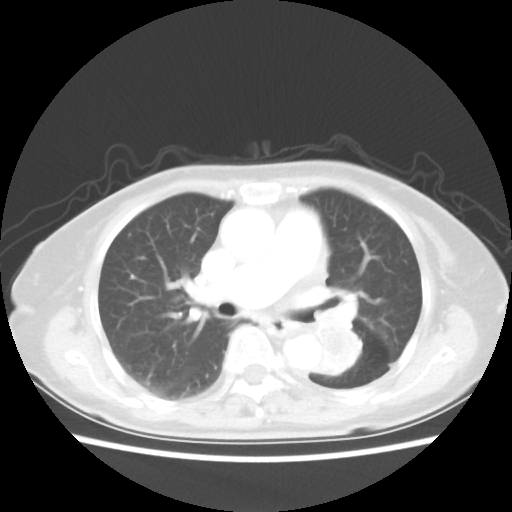
Chest CT, one axial slice. Position 29 of 50 along the scan axis. 80 kVp. Lung window (W 1500 / L -600 HU). 512 × 512 image matrix, field of view 335 × 335 mm. Patient: female, 81 years. From the clinical record (not read from this slice): clinical TNM (as recorded): T2 N0 M1a.
Structures marked on this image (rectangle marked by the reading radiologist):
- lung tumour (recorded histology: squamous cell carcinoma): bounding box <313,321,366,379> (left, top, right, bottom; pixels)